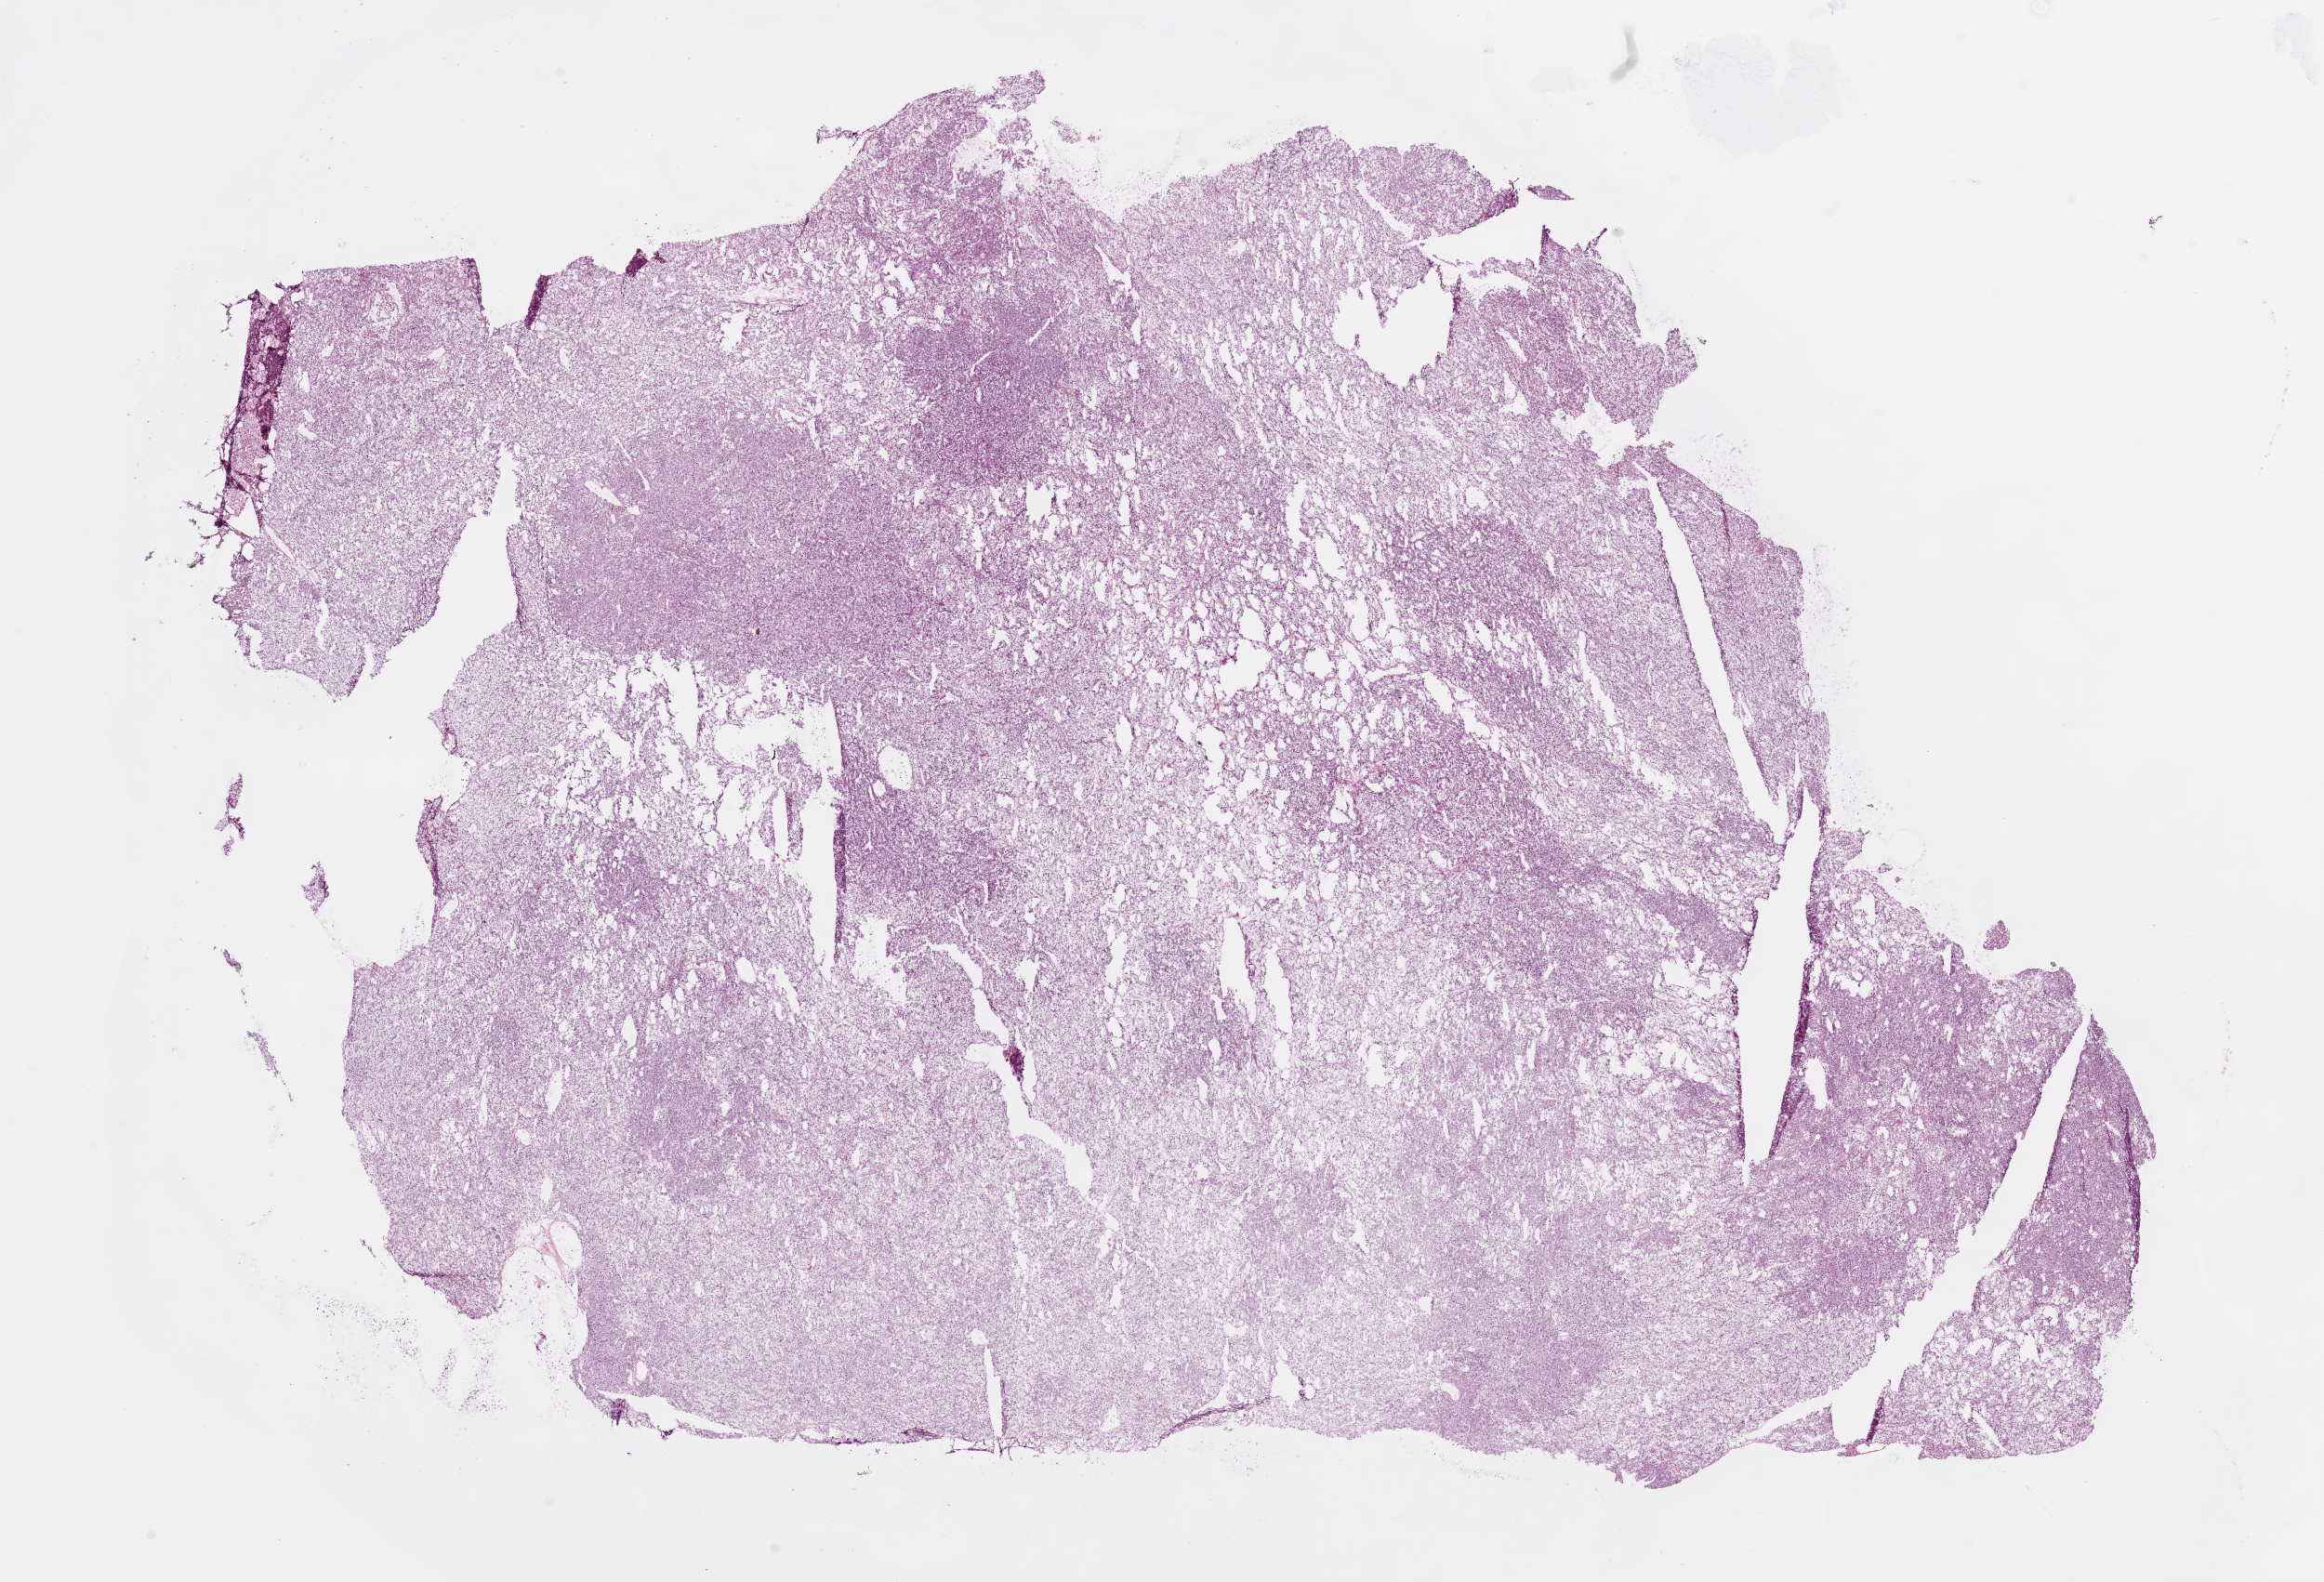
Whole-slide histology image, H&E — whole scanned area (about 20.1 x 13.7 mm, from a 20x scan) shown as a low-resolution overview. Frozen section from the top of the tissue portion. Sample: primary tumour, kidney. Male patient; age at initial diagnosis 77 years.
Histologic diagnosis: Clear cell adenocarcinoma, NOS.